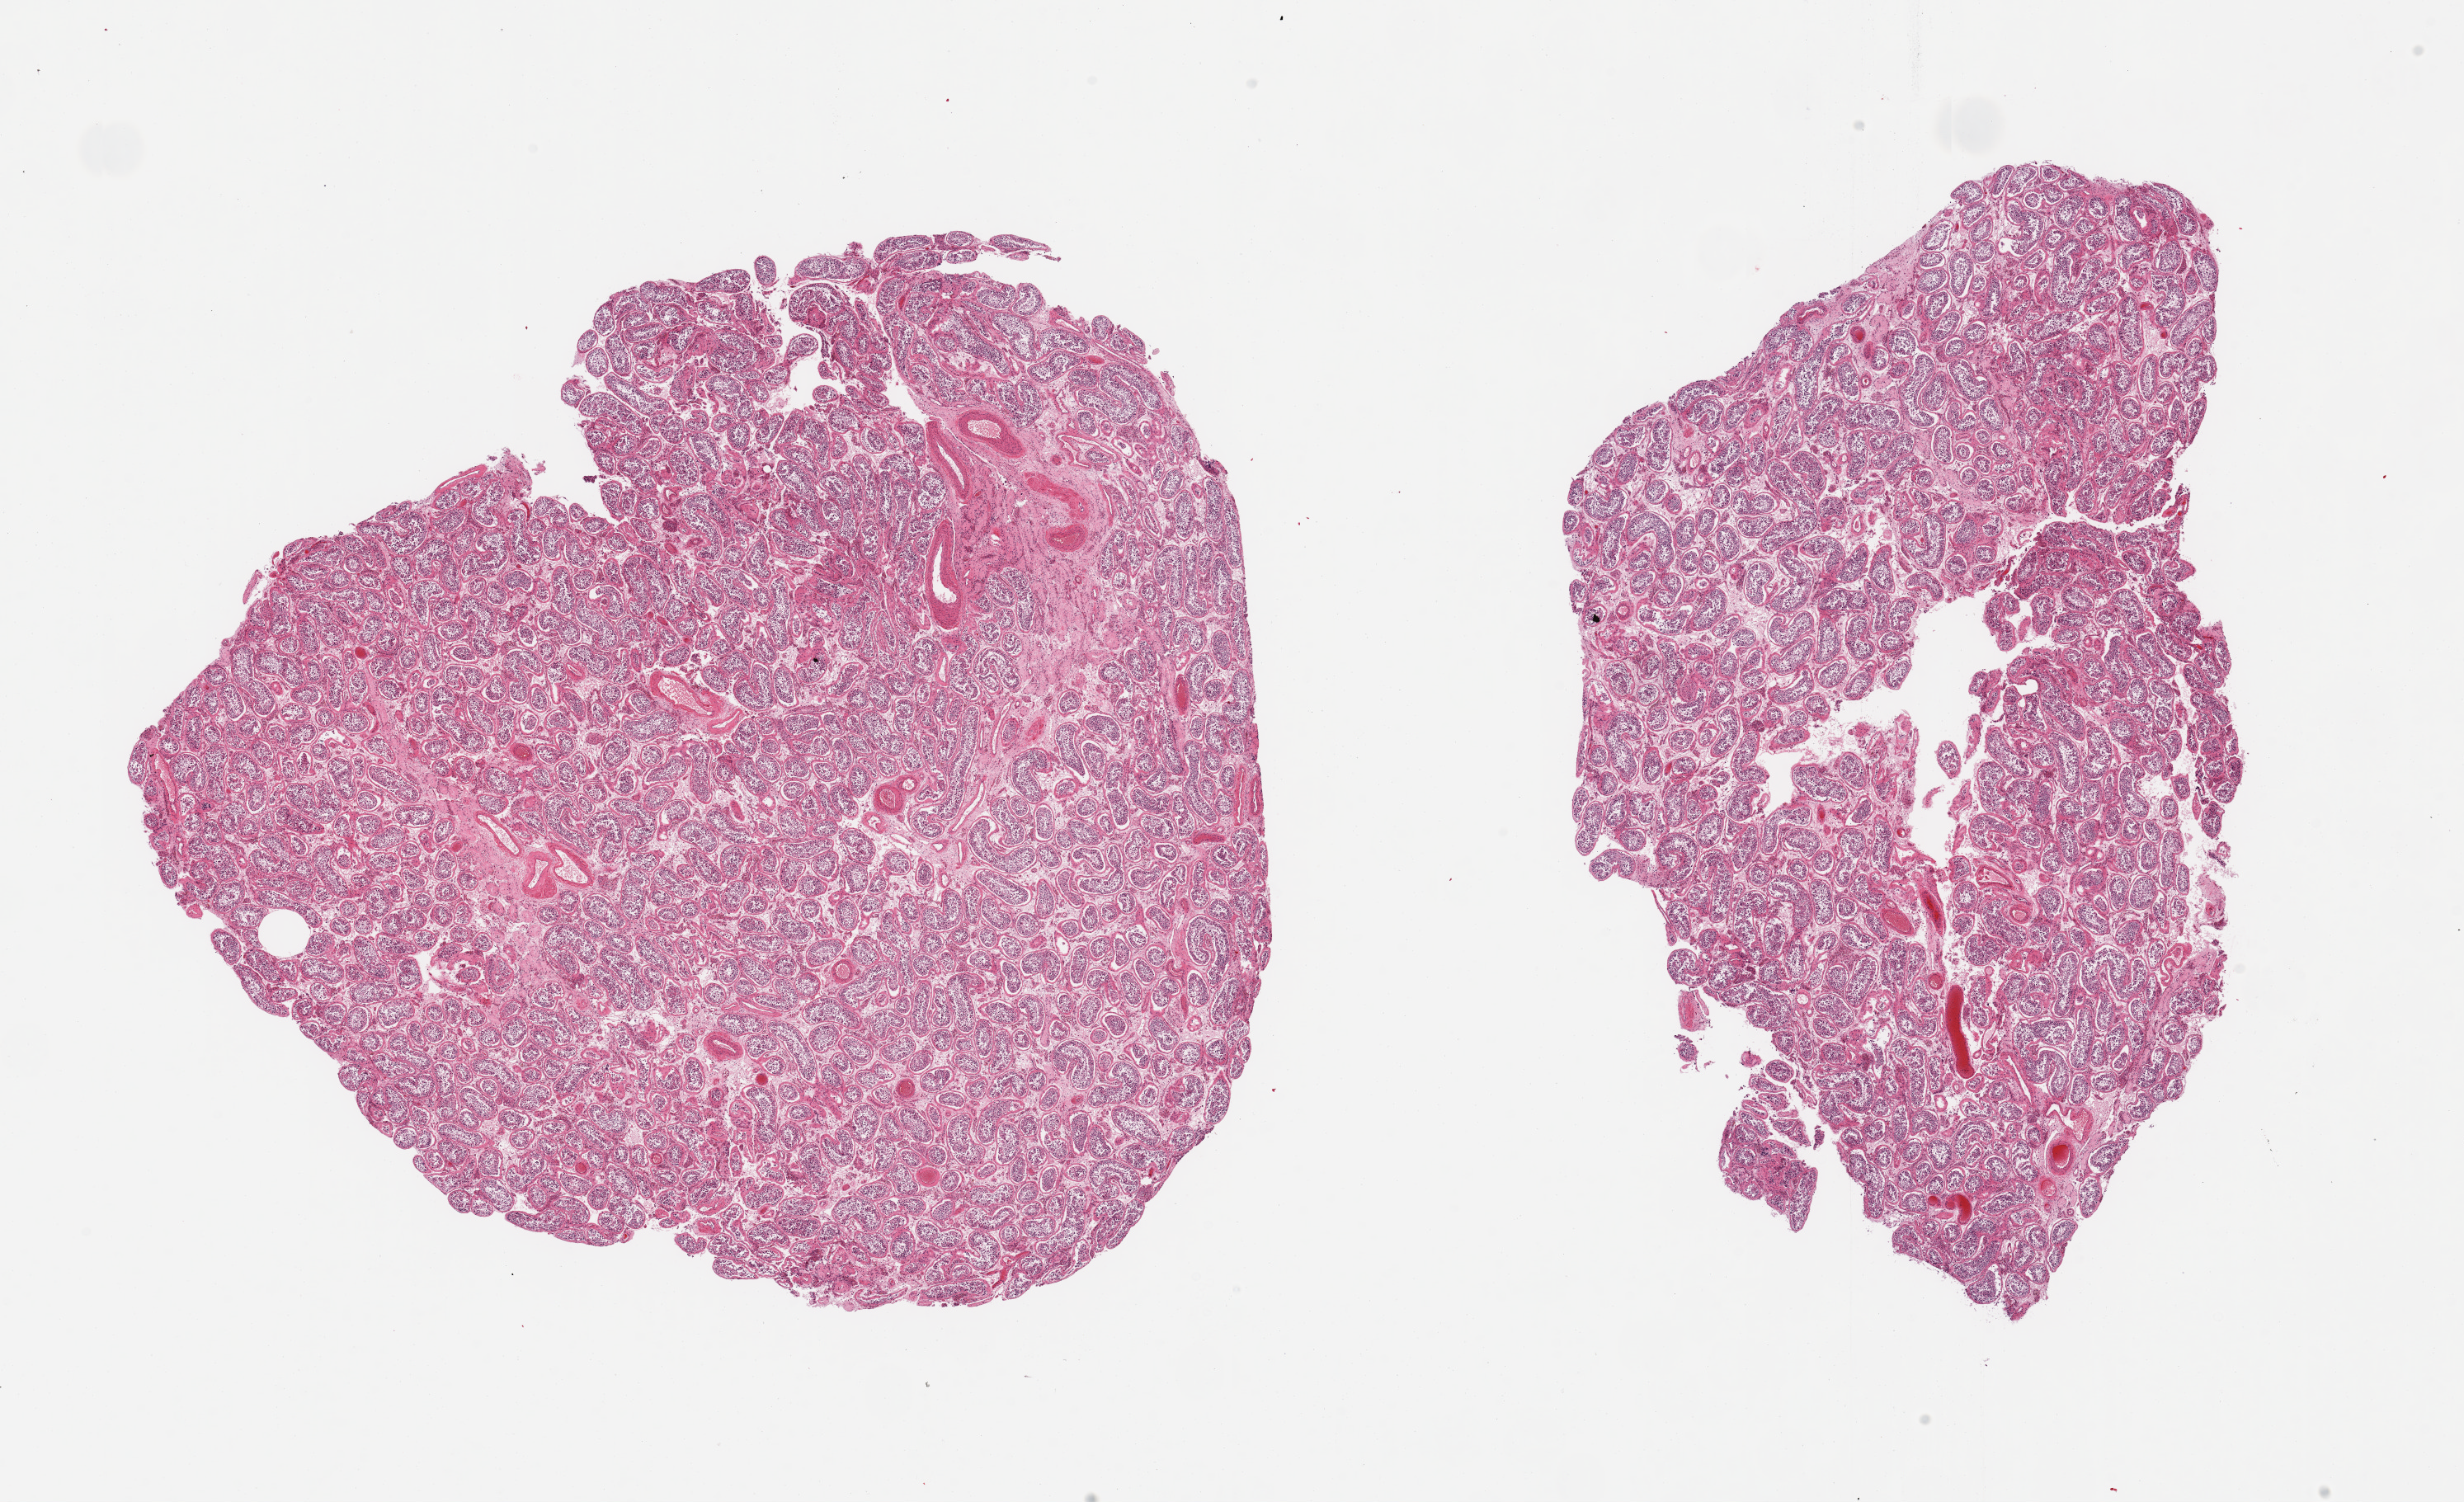
H&E whole-slide image, brightfield — low-resolution overview of the scanned area, about 23.6 x 14.4 mm. PAXgene-fixed, paraffin-embedded tissue. Section of testis (target tissue). Donor tissue sample. Donor: male.
* review note (as recorded): 2 pieces, spermatogenesis is present